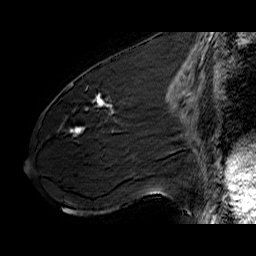
Breast MRI (dynamic contrast-enhanced), one sagittal slice. Position 29 of 60 along the scan axis. Dynamic contrast-enhanced series, time point 2 of 6 at this slice position (early post-contrast). 1.5 T. TE 6.4 ms, TR 32.9 ms. 4 mm slice thickness. 256 × 256 image matrix. Female patient. From the clinical record (not read from this slice): setting: breast cancer imaged before/during neoadjuvant chemotherapy; receptor status: HER2-positive.
Outlined on this slice (semi-automatic segmentation, software-assisted and operator-edited):
- analysis volume of interest (the breast-tissue region the enhancement analysis was run in; not a lesion): bounding box (x1, y1, x2, y2) in pixels: (61, 77, 141, 142)
- tumour enhancement mask (voxels above the 100 % enhancement threshold inside the analysis volume of interest): (70, 93, 115, 133)